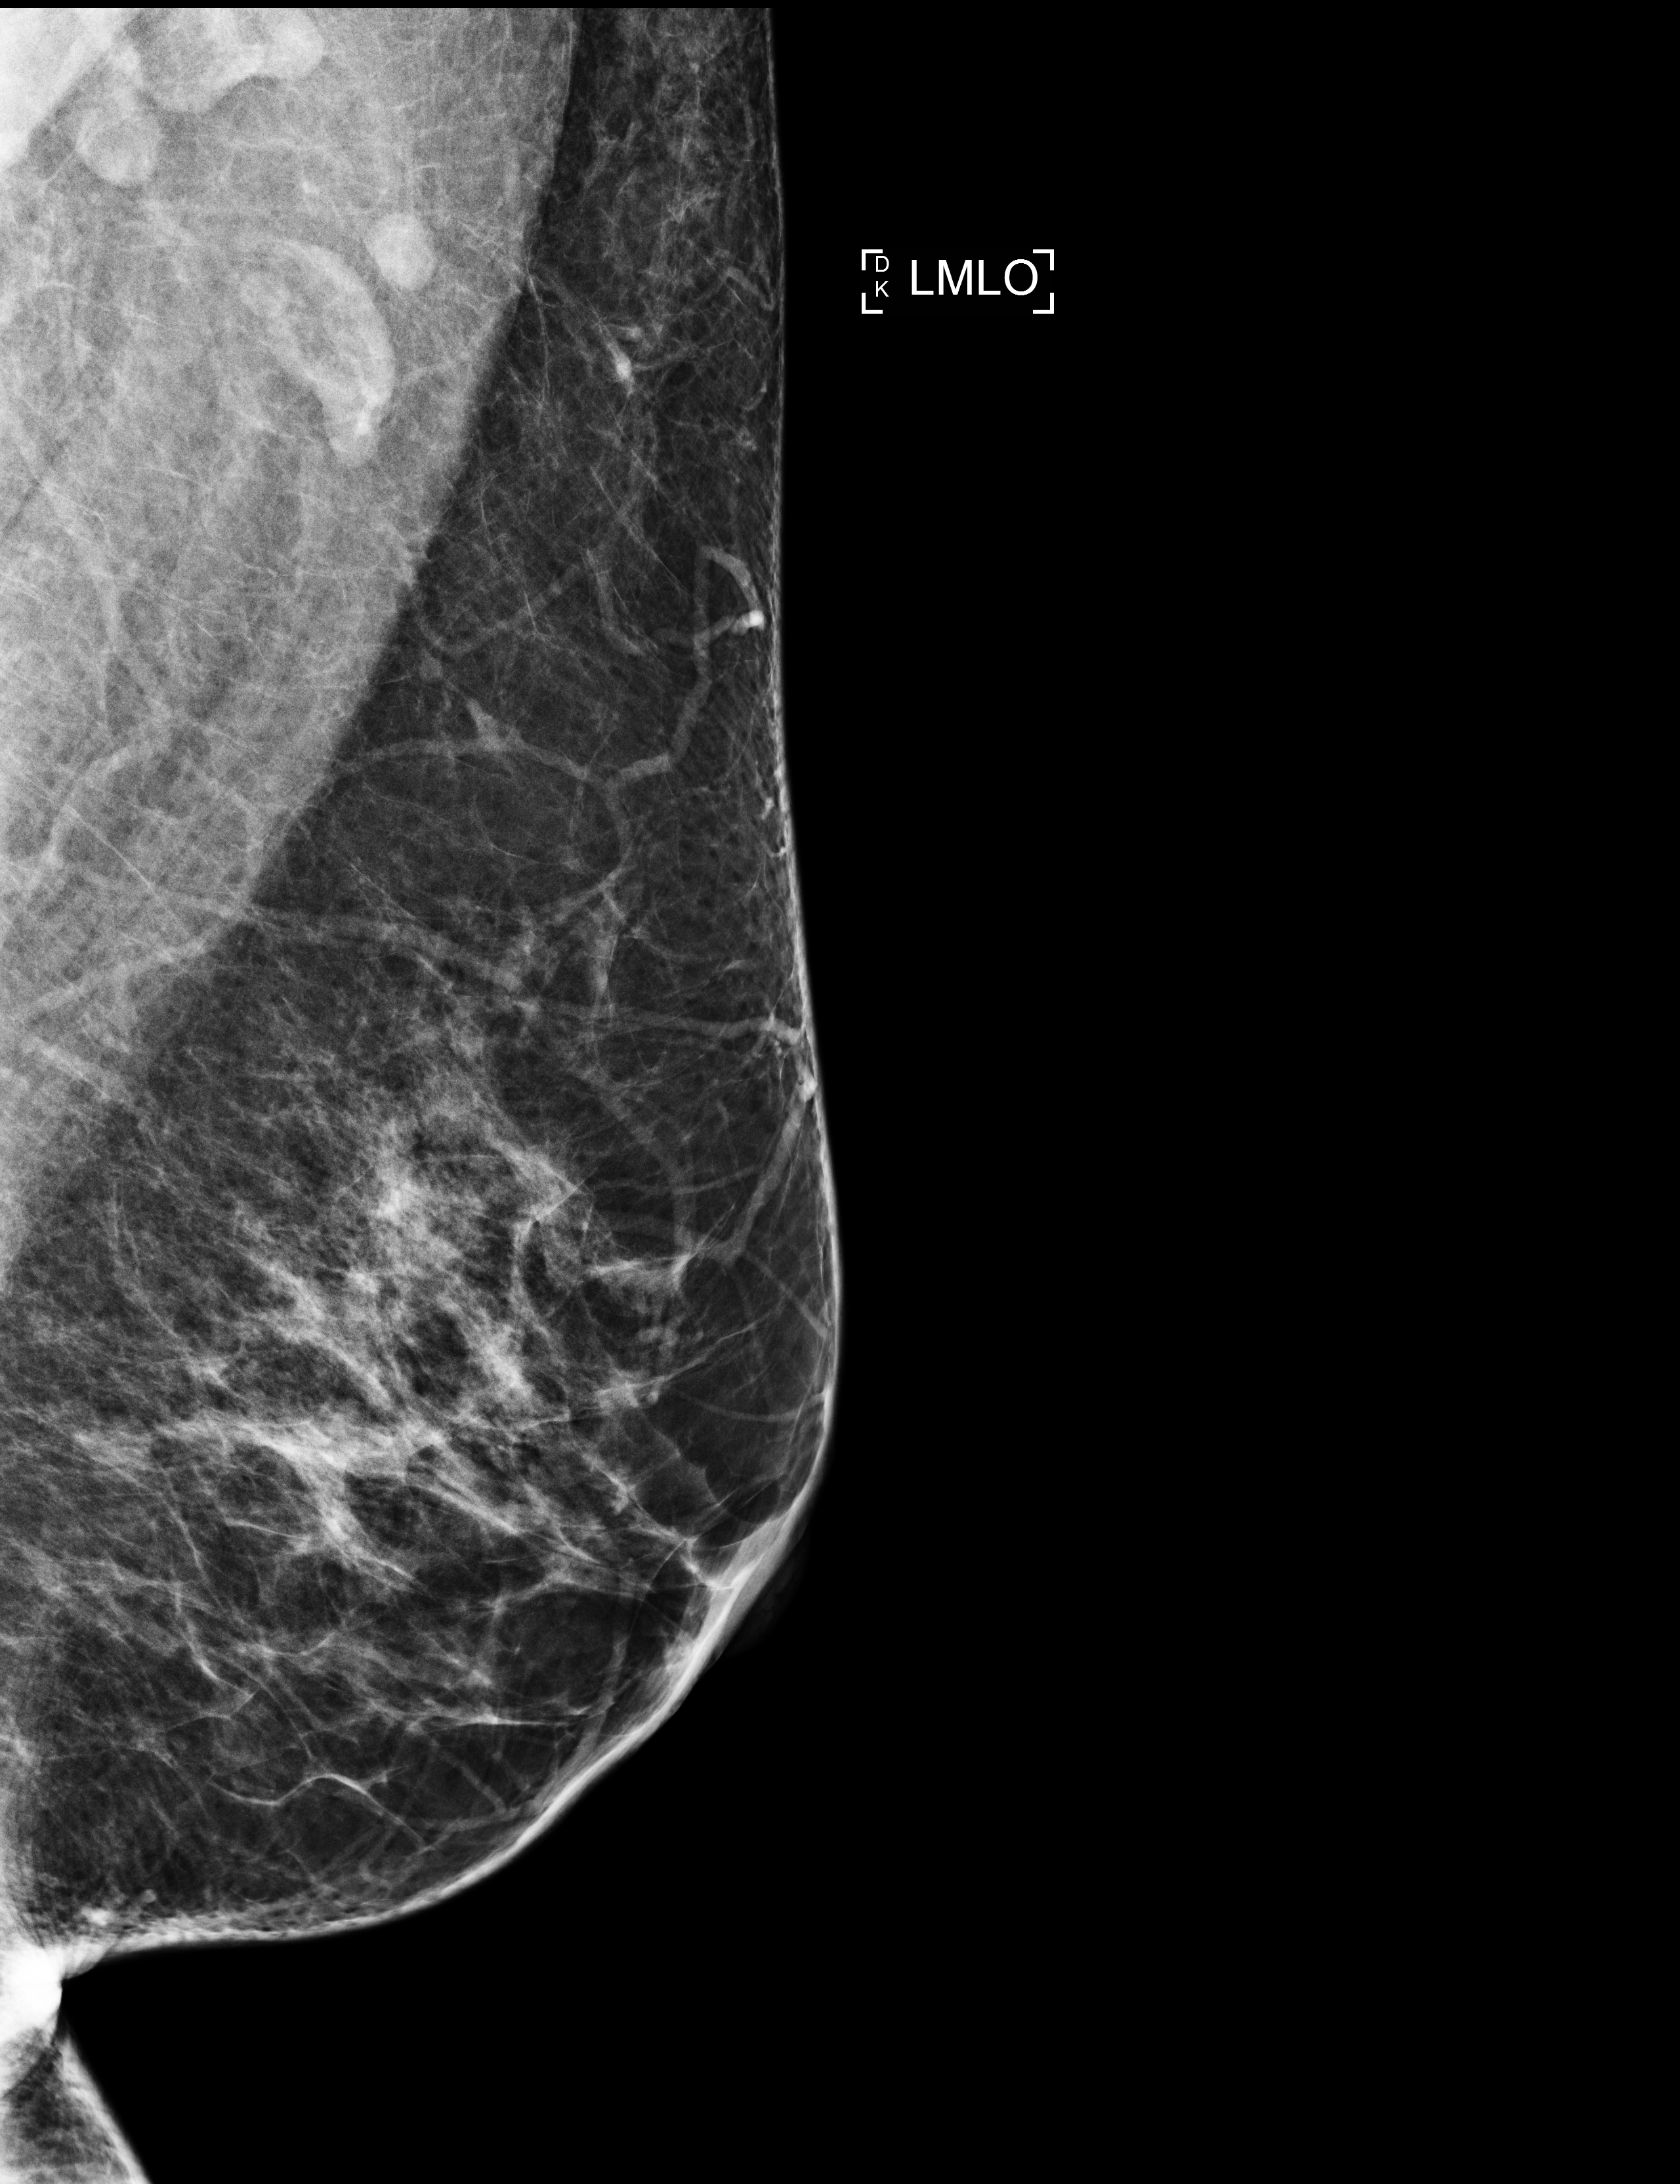
Annual screening mammography examination. Female patient, age 46 years.
Image type: full-field digital mammogram. Breast: left. Projection: medio-lateral oblique projection.